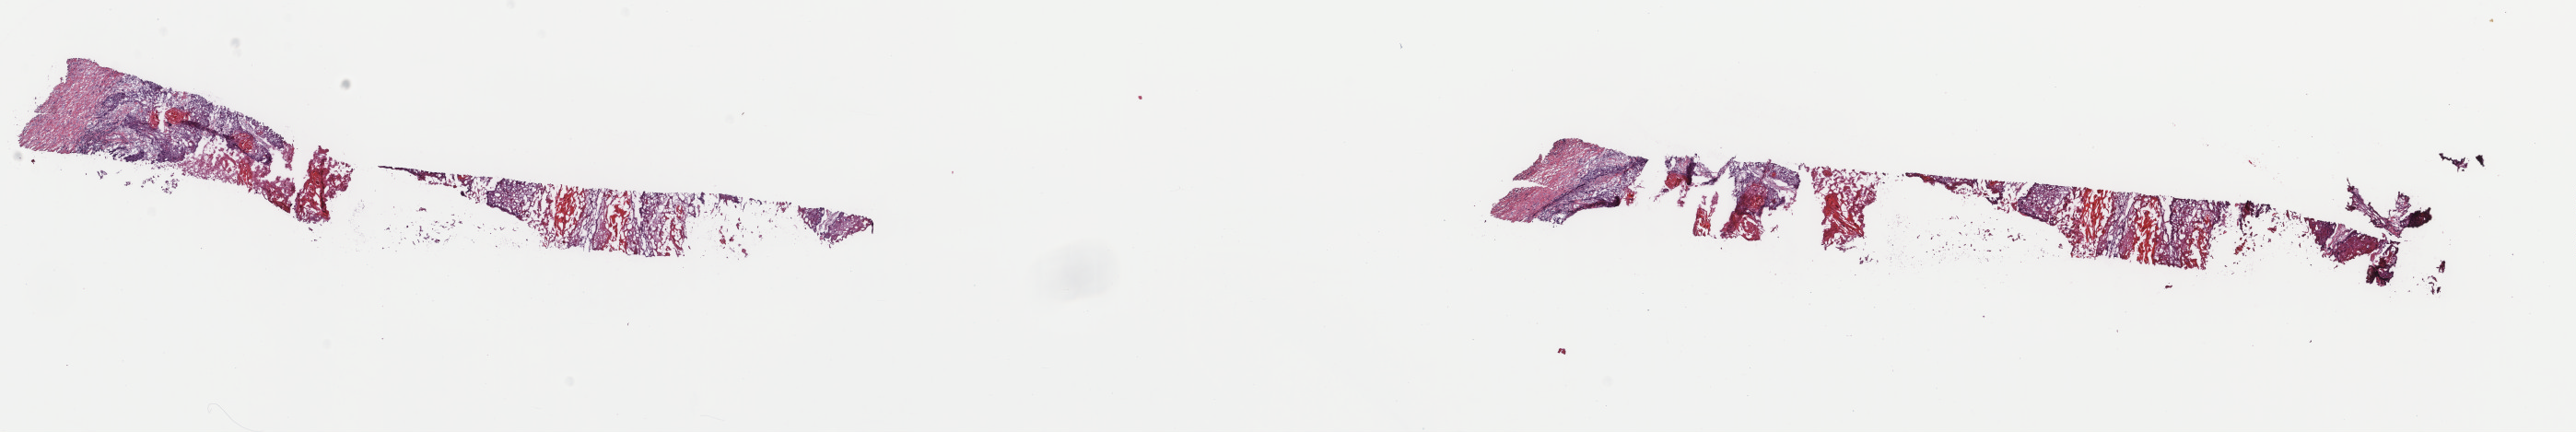
Digitized H&E tissue section (whole slide) — whole scanned area (about 22.2 x 3.7 mm, slide scanned at 40x) shown as a low-resolution overview; frozen section from the top of the tissue portion; sample: primary tumour, esophagus. Patient: male, age at initial diagnosis 60 years. Slide review estimates, as recorded: tumour cells 85%, tumour nuclei 80%.
Histologic diagnosis: Squamous cell carcinoma, NOS.